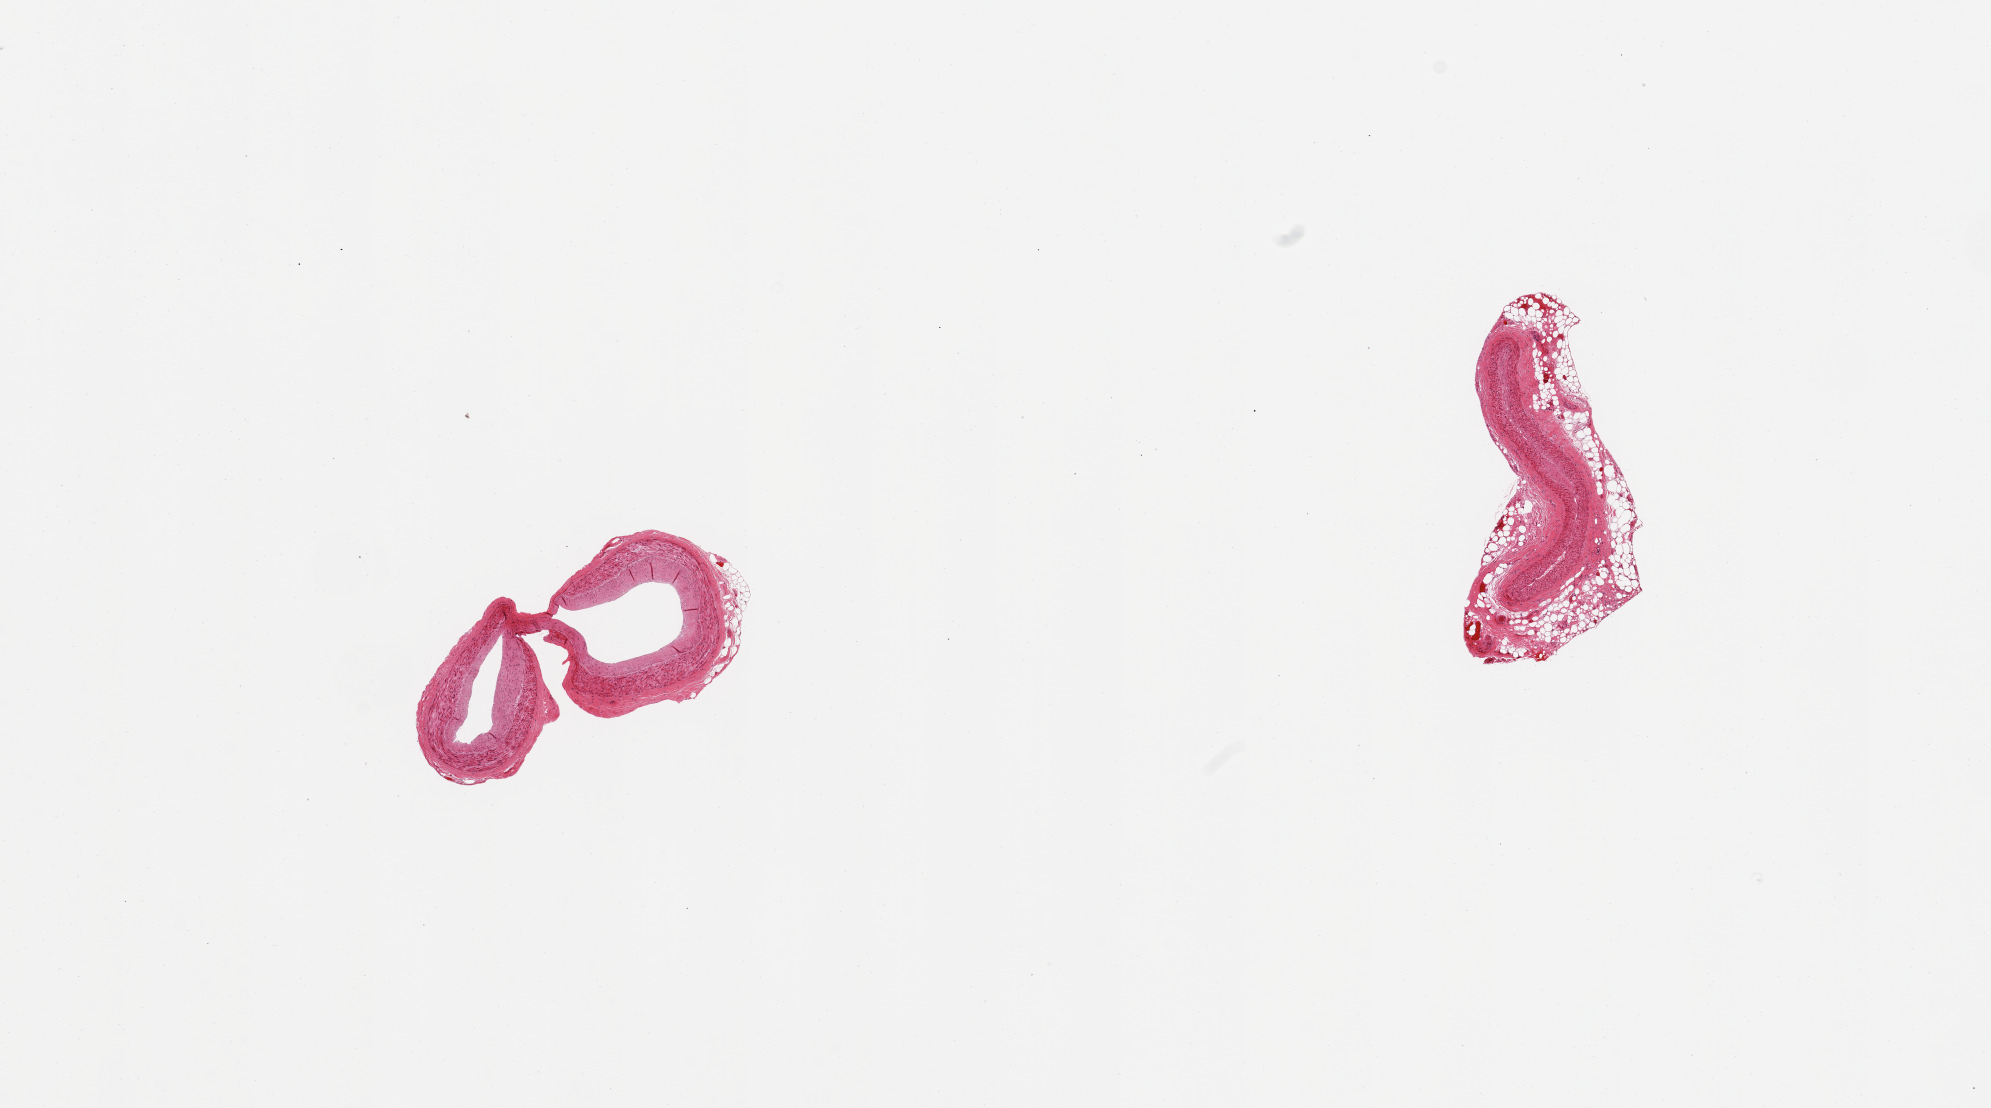
Whole-slide image, hematoxylin and eosin (H&E) stain, whole scanned area (about 15.8 x 8.8 mm, from a 20x scan) shown as a low-resolution overview; PAXgene-fixed, paraffin-embedded tissue; sampled site (target tissue): coronary artery; tissue donor sample. Female donor.
• review note (as recorded): 2 pieces; 1 piece has 40% external fat; no plaques